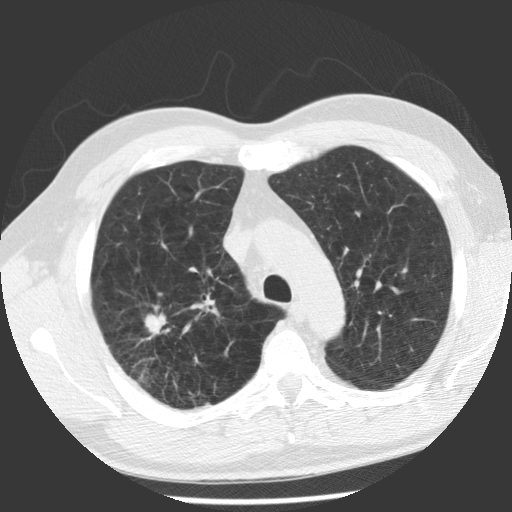
Axial slice from a low-dose chest CT screening exam. First (baseline) screen. Lung window (W 1500 / L -600 HU). Slice 84 of 112 in the series. Male, age 62 years at enrolment. Former smoker at enrolment.
- Lesion marked by an expert reader, bounding box (x1, y1, x2, y2) in pixels: (115, 301, 193, 378).
- The screening reader recorded 2 non-calcified nodules or masses ≥4 mm on this exam (right upper lobe, right upper lobe); which of them this box marks is not recorded.
- Official screen result: positive, change unspecified: nodule(s) >= 4 mm or enlarging nodule(s), mass(es), or other non-specific abnormalities suspicious for lung cancer.
- Later outcome: lung cancer diagnosed 71 days after this screen — adenocarcinoma, NOS, right upper lobe, poorly differentiated (G3), stage IV (AJCC 6th edition), 30 mm at pathology.